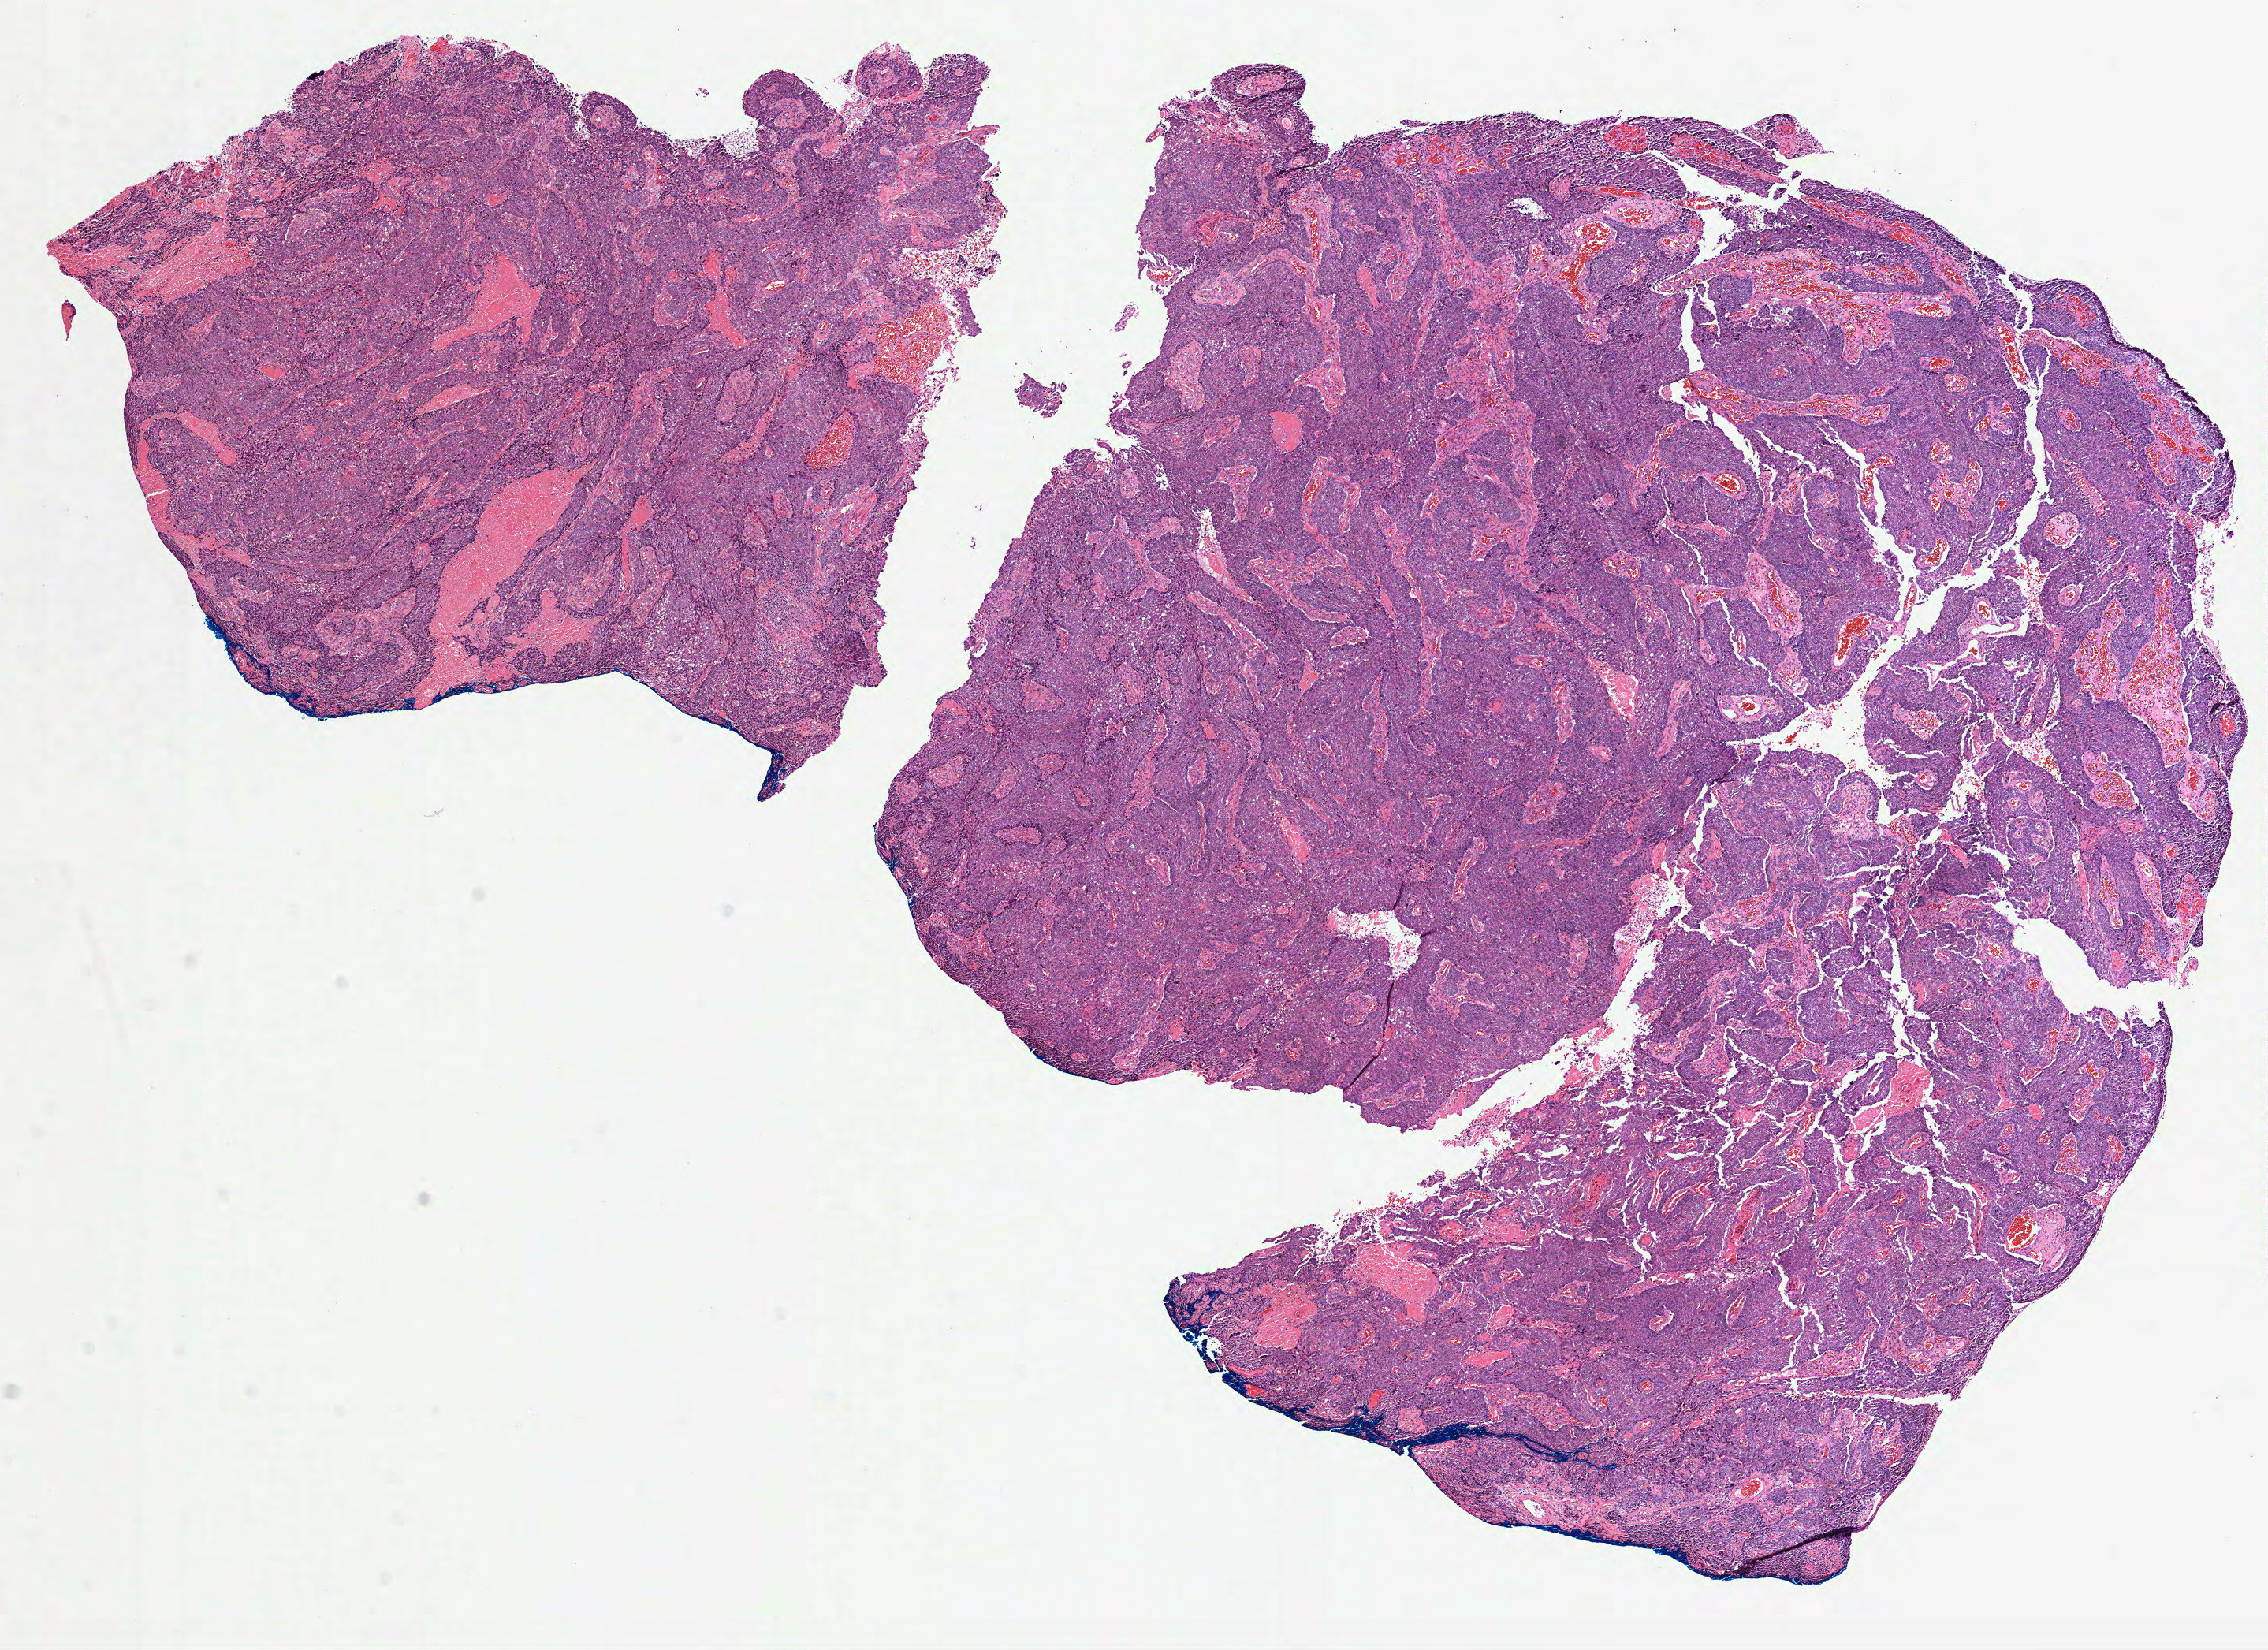
H&E whole-slide image, whole scanned area (about 11.6 x 8.4 mm) shown as a low-resolution overview. Formalin-fixed paraffin-embedded (FFPE) diagnostic section. Sample: primary tumour, cervix. Female patient; age at initial diagnosis 78 years. Histologic grade: G3 (poorly differentiated).
FIGO stage: IB2. Histologic diagnosis: Squamous cell carcinoma, NOS (cervix uteri). Lymph nodes positive (case pathology): 0 of 30 examined.